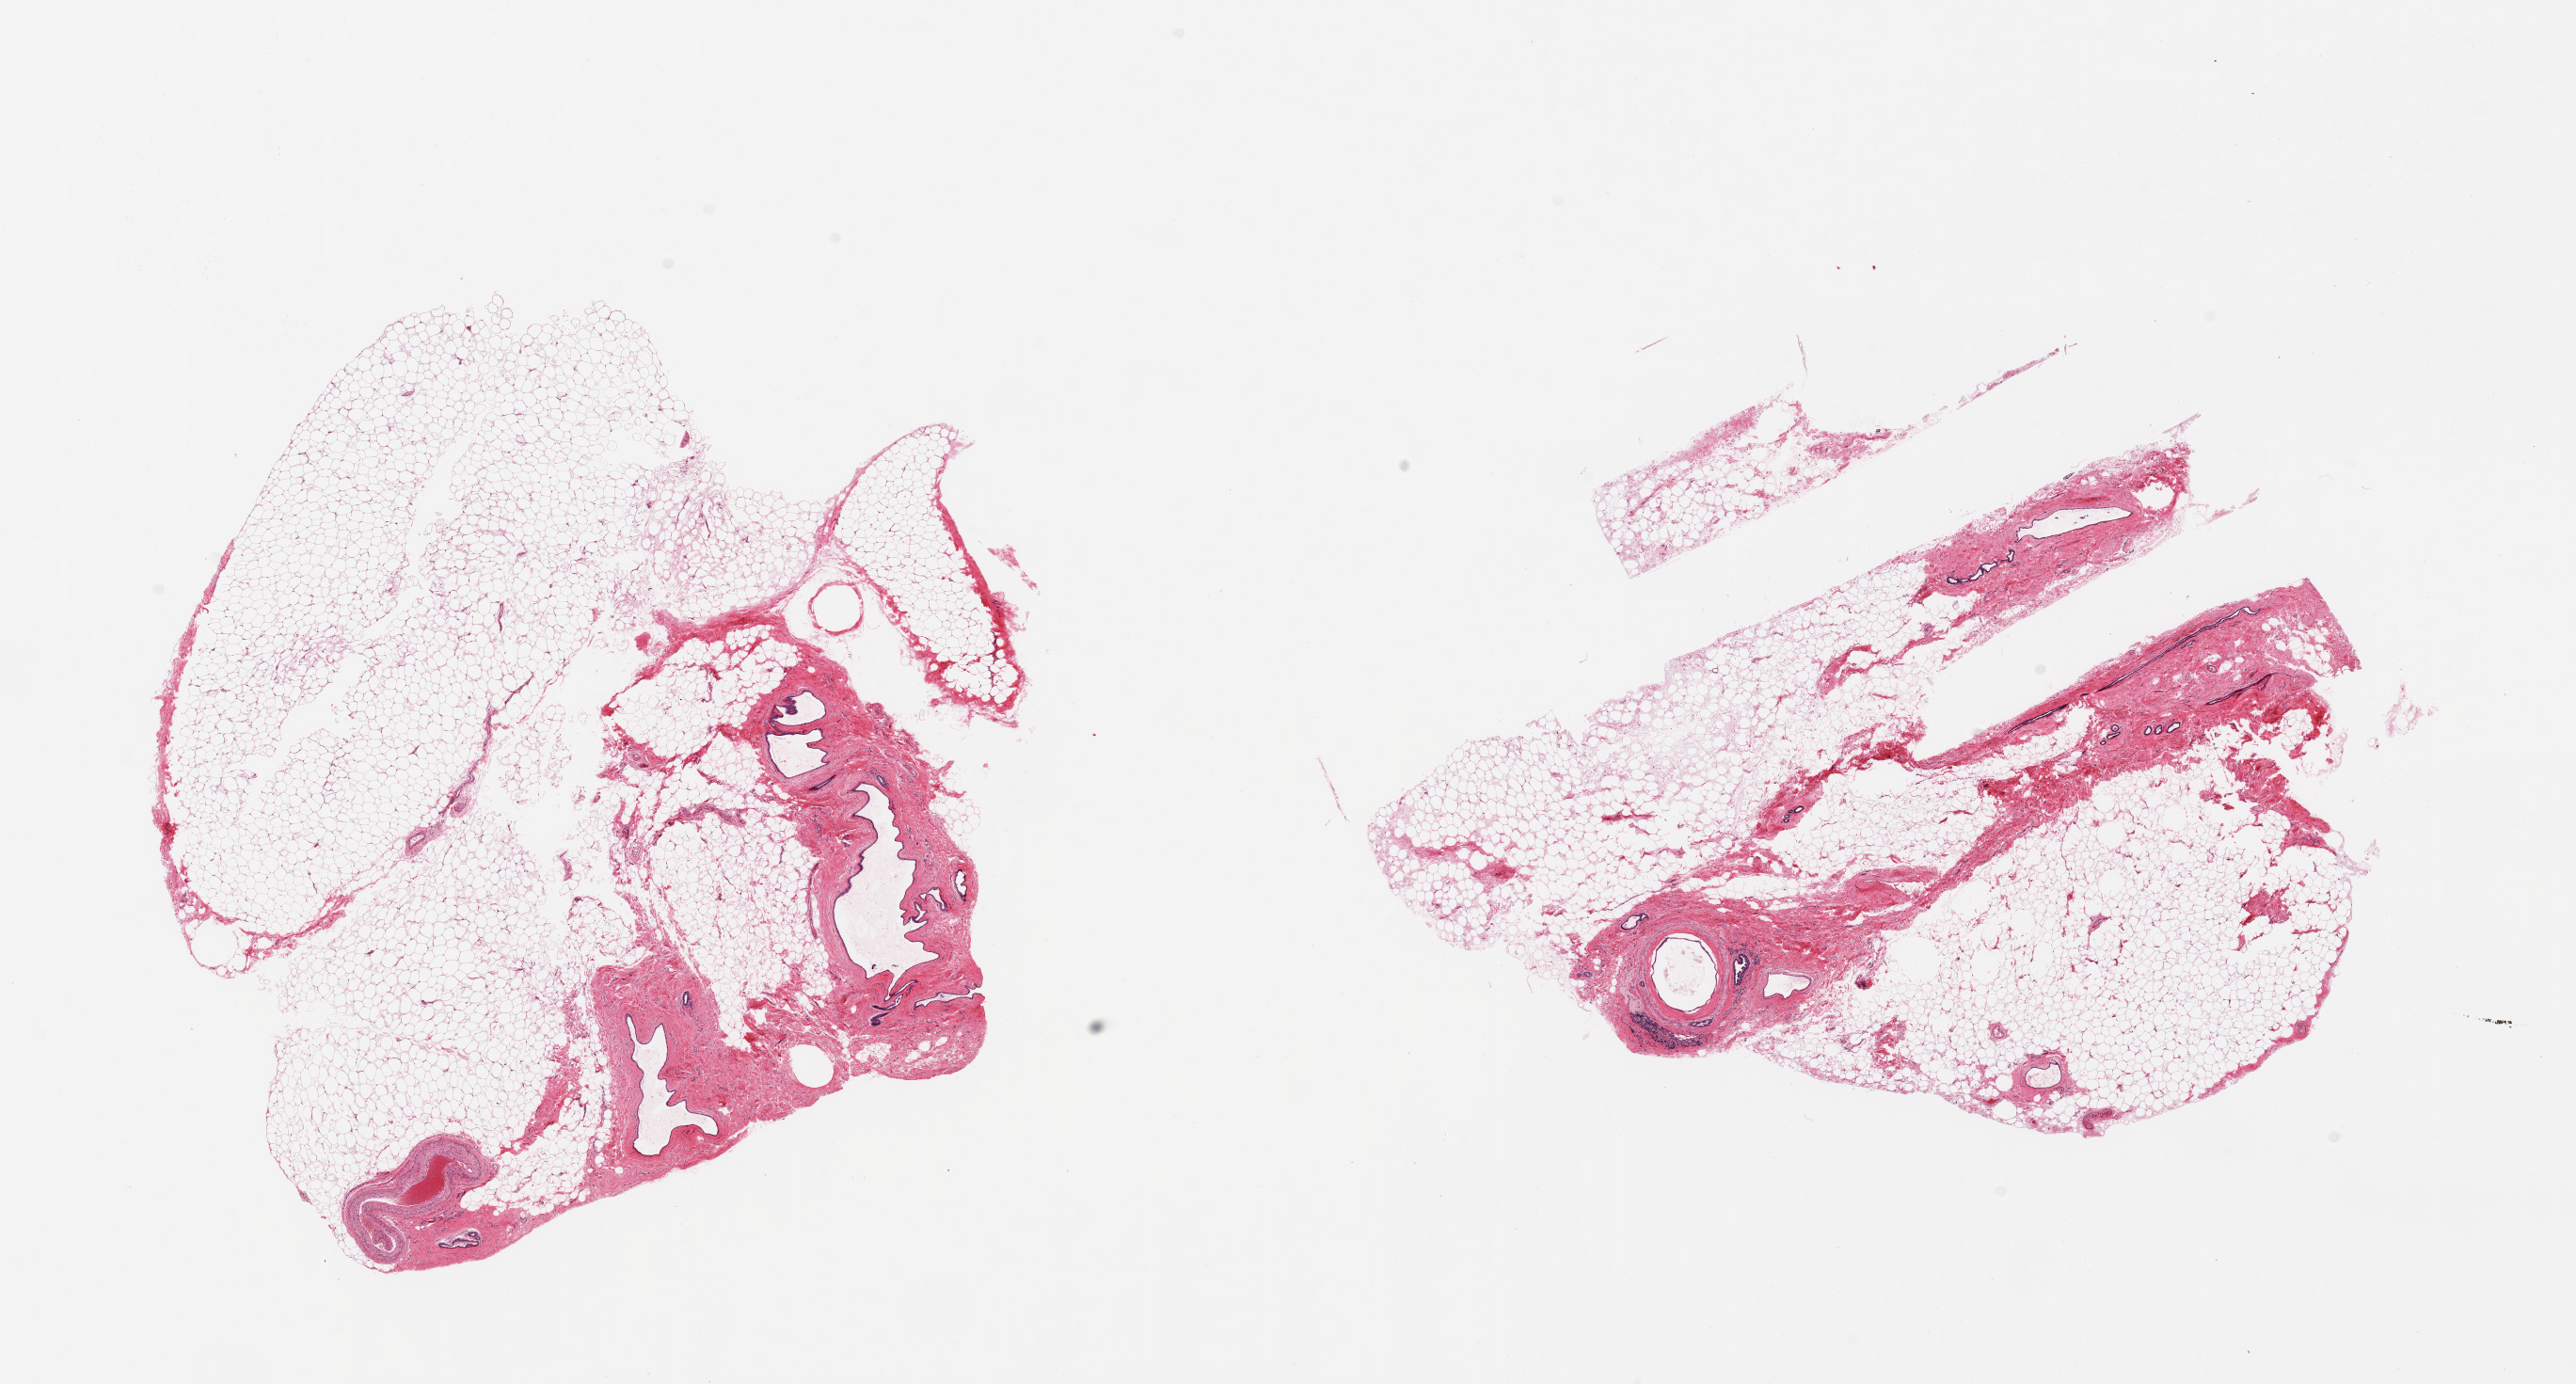
Digitized haematoxylin and eosin-stained section, brightfield, whole scanned area (about 21.7 x 11.6 mm, from a 20x scan) shown as a low-resolution overview. PAXgene-fixed paraffin-embedded (PFPE) section. Target tissue: breast. Tissue donor sample. Donor sex: female.
Reviewer comment on this tissue sample: 2 pieces; atrophic mammary tissue with dilated ducts; 60% fat.